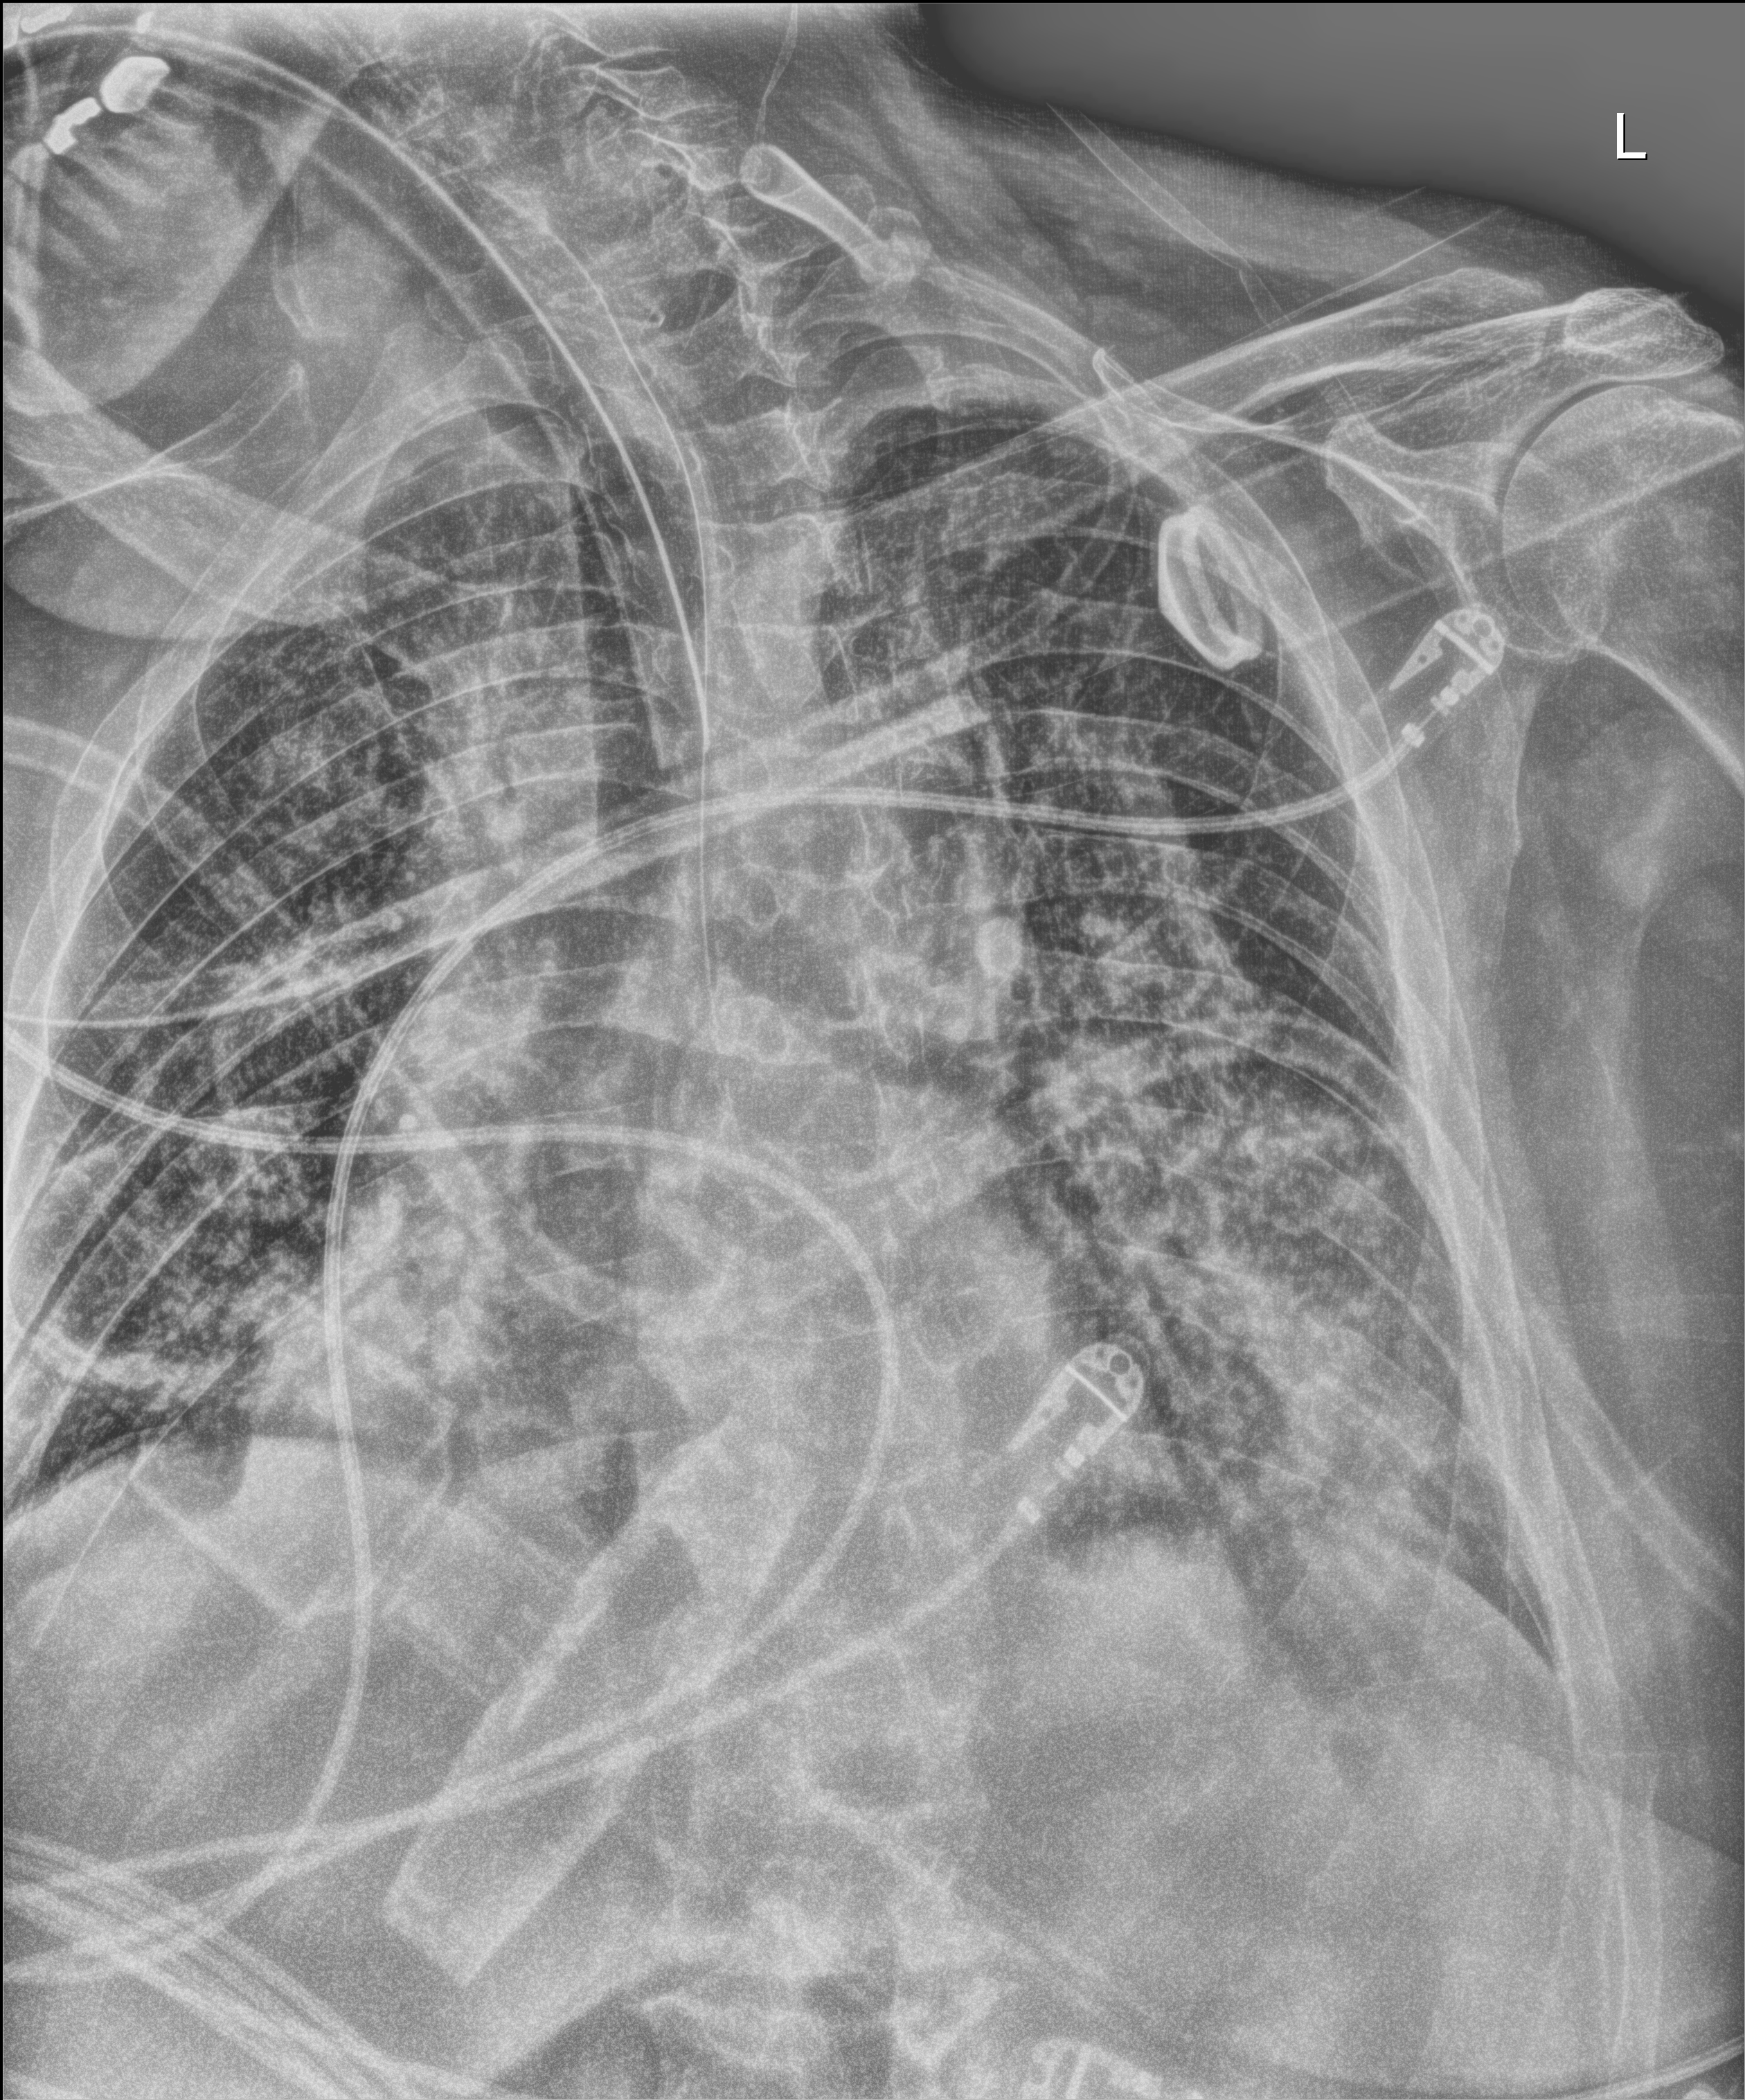
Chest radiograph; anteroposterior (AP) projection. Patient hospitalised with COVID-19; male, aged 60–74 years.
From the hospital-stay record, not from the radiograph (when in the stay this image was taken is not recorded): mechanically ventilated during this hospital stay: yes; admitted to intensive care during this hospital stay: yes; diabetes (admission record): no.